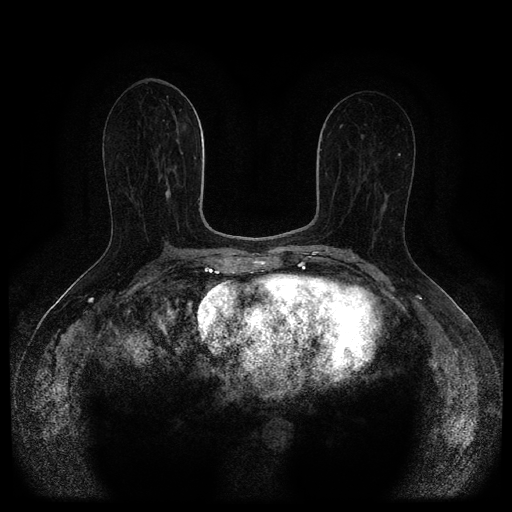
Breast MRI (dynamic contrast-enhanced, multi-phase), one axial slice. Position 52 of 116 along the scan axis. Dynamic contrast-enhanced series, time point 2 of 5 at this slice position (early post-contrast). 1.5 T. TE 2.7 ms, TR 5.4 ms. 2 mm slice thickness. 512 × 512 image matrix. Patient: female, 71 years.
Annotated regions visible in this slice (semi-automatically segmented with operator editing):
- breast lesion (labelled 'tumour' in the annotation; benign lesions carry a separate 'benign' label): bounding box (x1, y1, x2, y2) in pixels: (165, 188, 171, 198)